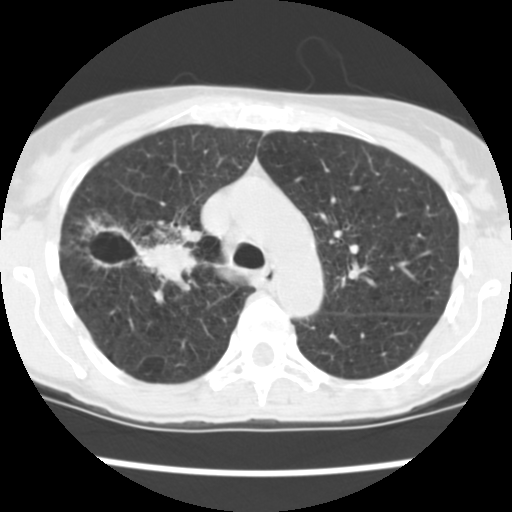
Low-dose screening chest CT, one axial slice. Slice 173 of 252 in the series (ordered by position). Reconstruction kernel STANDARD. Lung window (W 1500 / L -600 HU). 512 × 512 image matrix, field of view 276 × 276 mm.
Outlined on this slice (expert manual segmentation):
- lesion 2 (tumor, lower lobe of right lung): box from (x=88, y=221) to (x=201, y=288) px